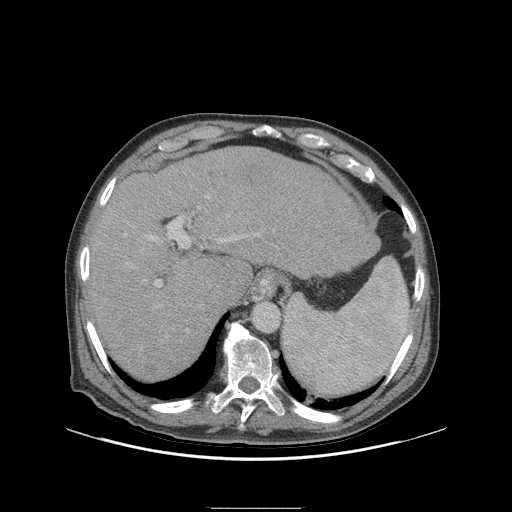
Contrast-enhanced abdominal CT (liver protocol), one axial slice; position 74 of 105 along the scan axis; 140 kVp; soft-tissue window (W 400 / L 40 HU); 2.5 mm slice thickness; 512 × 512 image matrix. From the clinical record (not read from this slice): diagnosis: hepatocellular carcinoma (patient treated with transarterial chemoembolisation; whether this scan precedes or follows treatment is not stated here); TNM stage (as recorded): Stage-I; Child-Pugh class: A; tumour size: 5.1 cm.
Outlined on this slice (semi-automatic segmentation, software-assisted and operator-edited):
- liver parenchyma outside the tumour (the mass and vessels are separate outlines, so this box may not span the whole liver): box from (x=88, y=146) to (x=378, y=380) px
- liver vessels: (x=125, y=196)–(x=256, y=287)